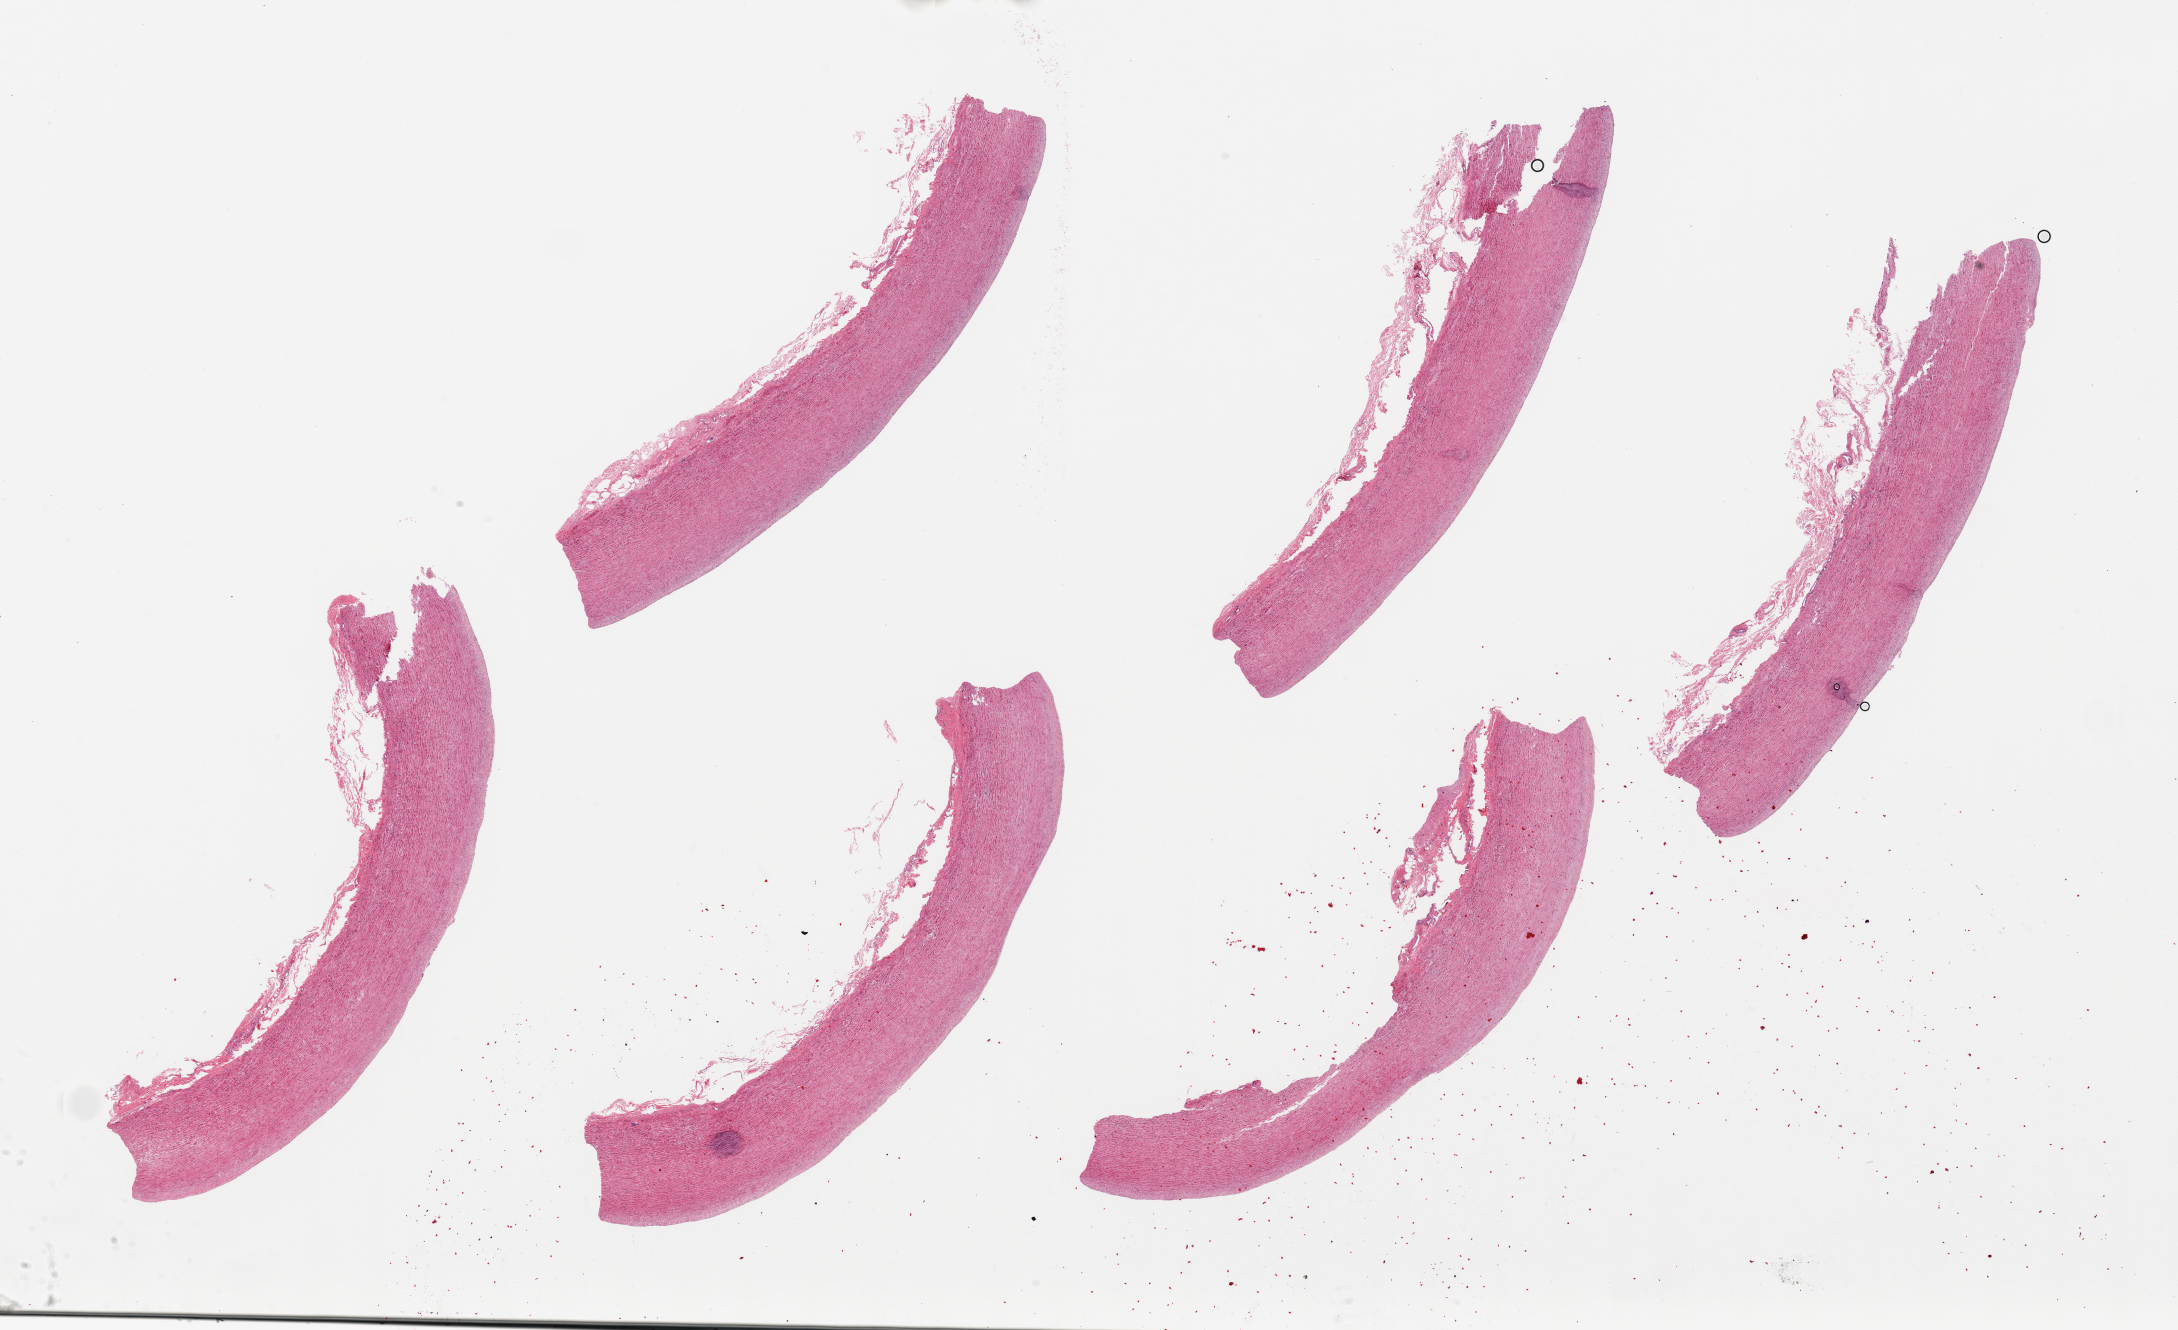
Digitized haematoxylin and eosin-stained section — whole scanned area (about 34.5 x 21.0 mm) shown as a low-resolution overview; PAXgene-fixed paraffin-embedded (PFPE) section; sampled site (target tissue): aorta; tissue donor sample.
- reviewer comment on this tissue sample: 6 pieces ~10x2mm